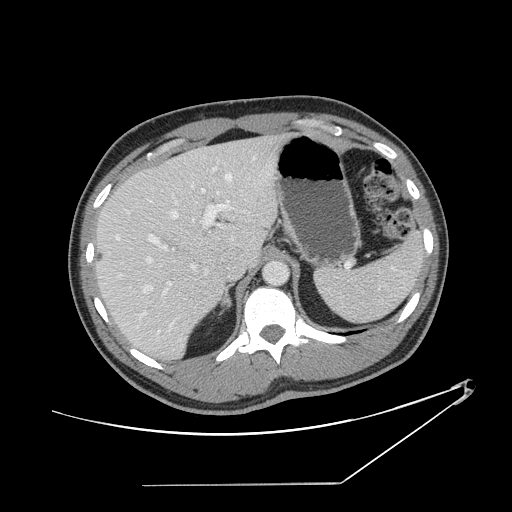
Contrast-enhanced abdominal CT, one axial slice; position 100 of 152 along the scan axis; 120 kVp; intravenous contrast given; soft-tissue window (W 400 / L 40 HU); 2.5 mm slice thickness; 512 × 512 image matrix, field of view 432 × 432 mm. Male patient, age 45 years. Case-level facts recorded for this patient, not image findings: diagnosis: colorectal cancer liver metastases, imaged before liver resection; multiple liver metastases: no; largest metastasis: 1 cm; chemotherapy before resection: yes.
Outlined on this slice (outlined manually by an expert reader):
- hepatic veins: box from (x=114, y=156) to (x=256, y=328) px
- liver: (x=98, y=136)–(x=283, y=358)
- planned liver remnant (the part of the liver to remain after resection): (x=98, y=154)–(x=231, y=358)
- portal vein (with intrahepatic branches): (x=136, y=168)–(x=231, y=336)